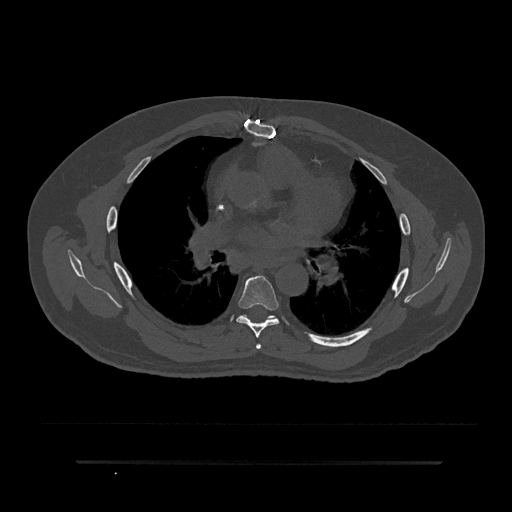
CT including the spine, one axial slice; slice 519 of 797 in the series (ordered by position); reconstruction kernel Br40s/3; bone window (W 1800 / L 400 HU); 512 × 512 image matrix, field of view 464 × 464 mm. Patient: male, 59 years. From the clinical record (not read from this slice): primary cancer: bile ducts; vertebrae with lytic lesions (as recorded): T10.
Annotated regions visible in this slice (semi-automatic segmentation, software-assisted and operator-edited):
- T5 vertebra: bounding box <256,344,261,349> (left, top, right, bottom; pixels)
- T6 vertebra: <236,276,280,338>